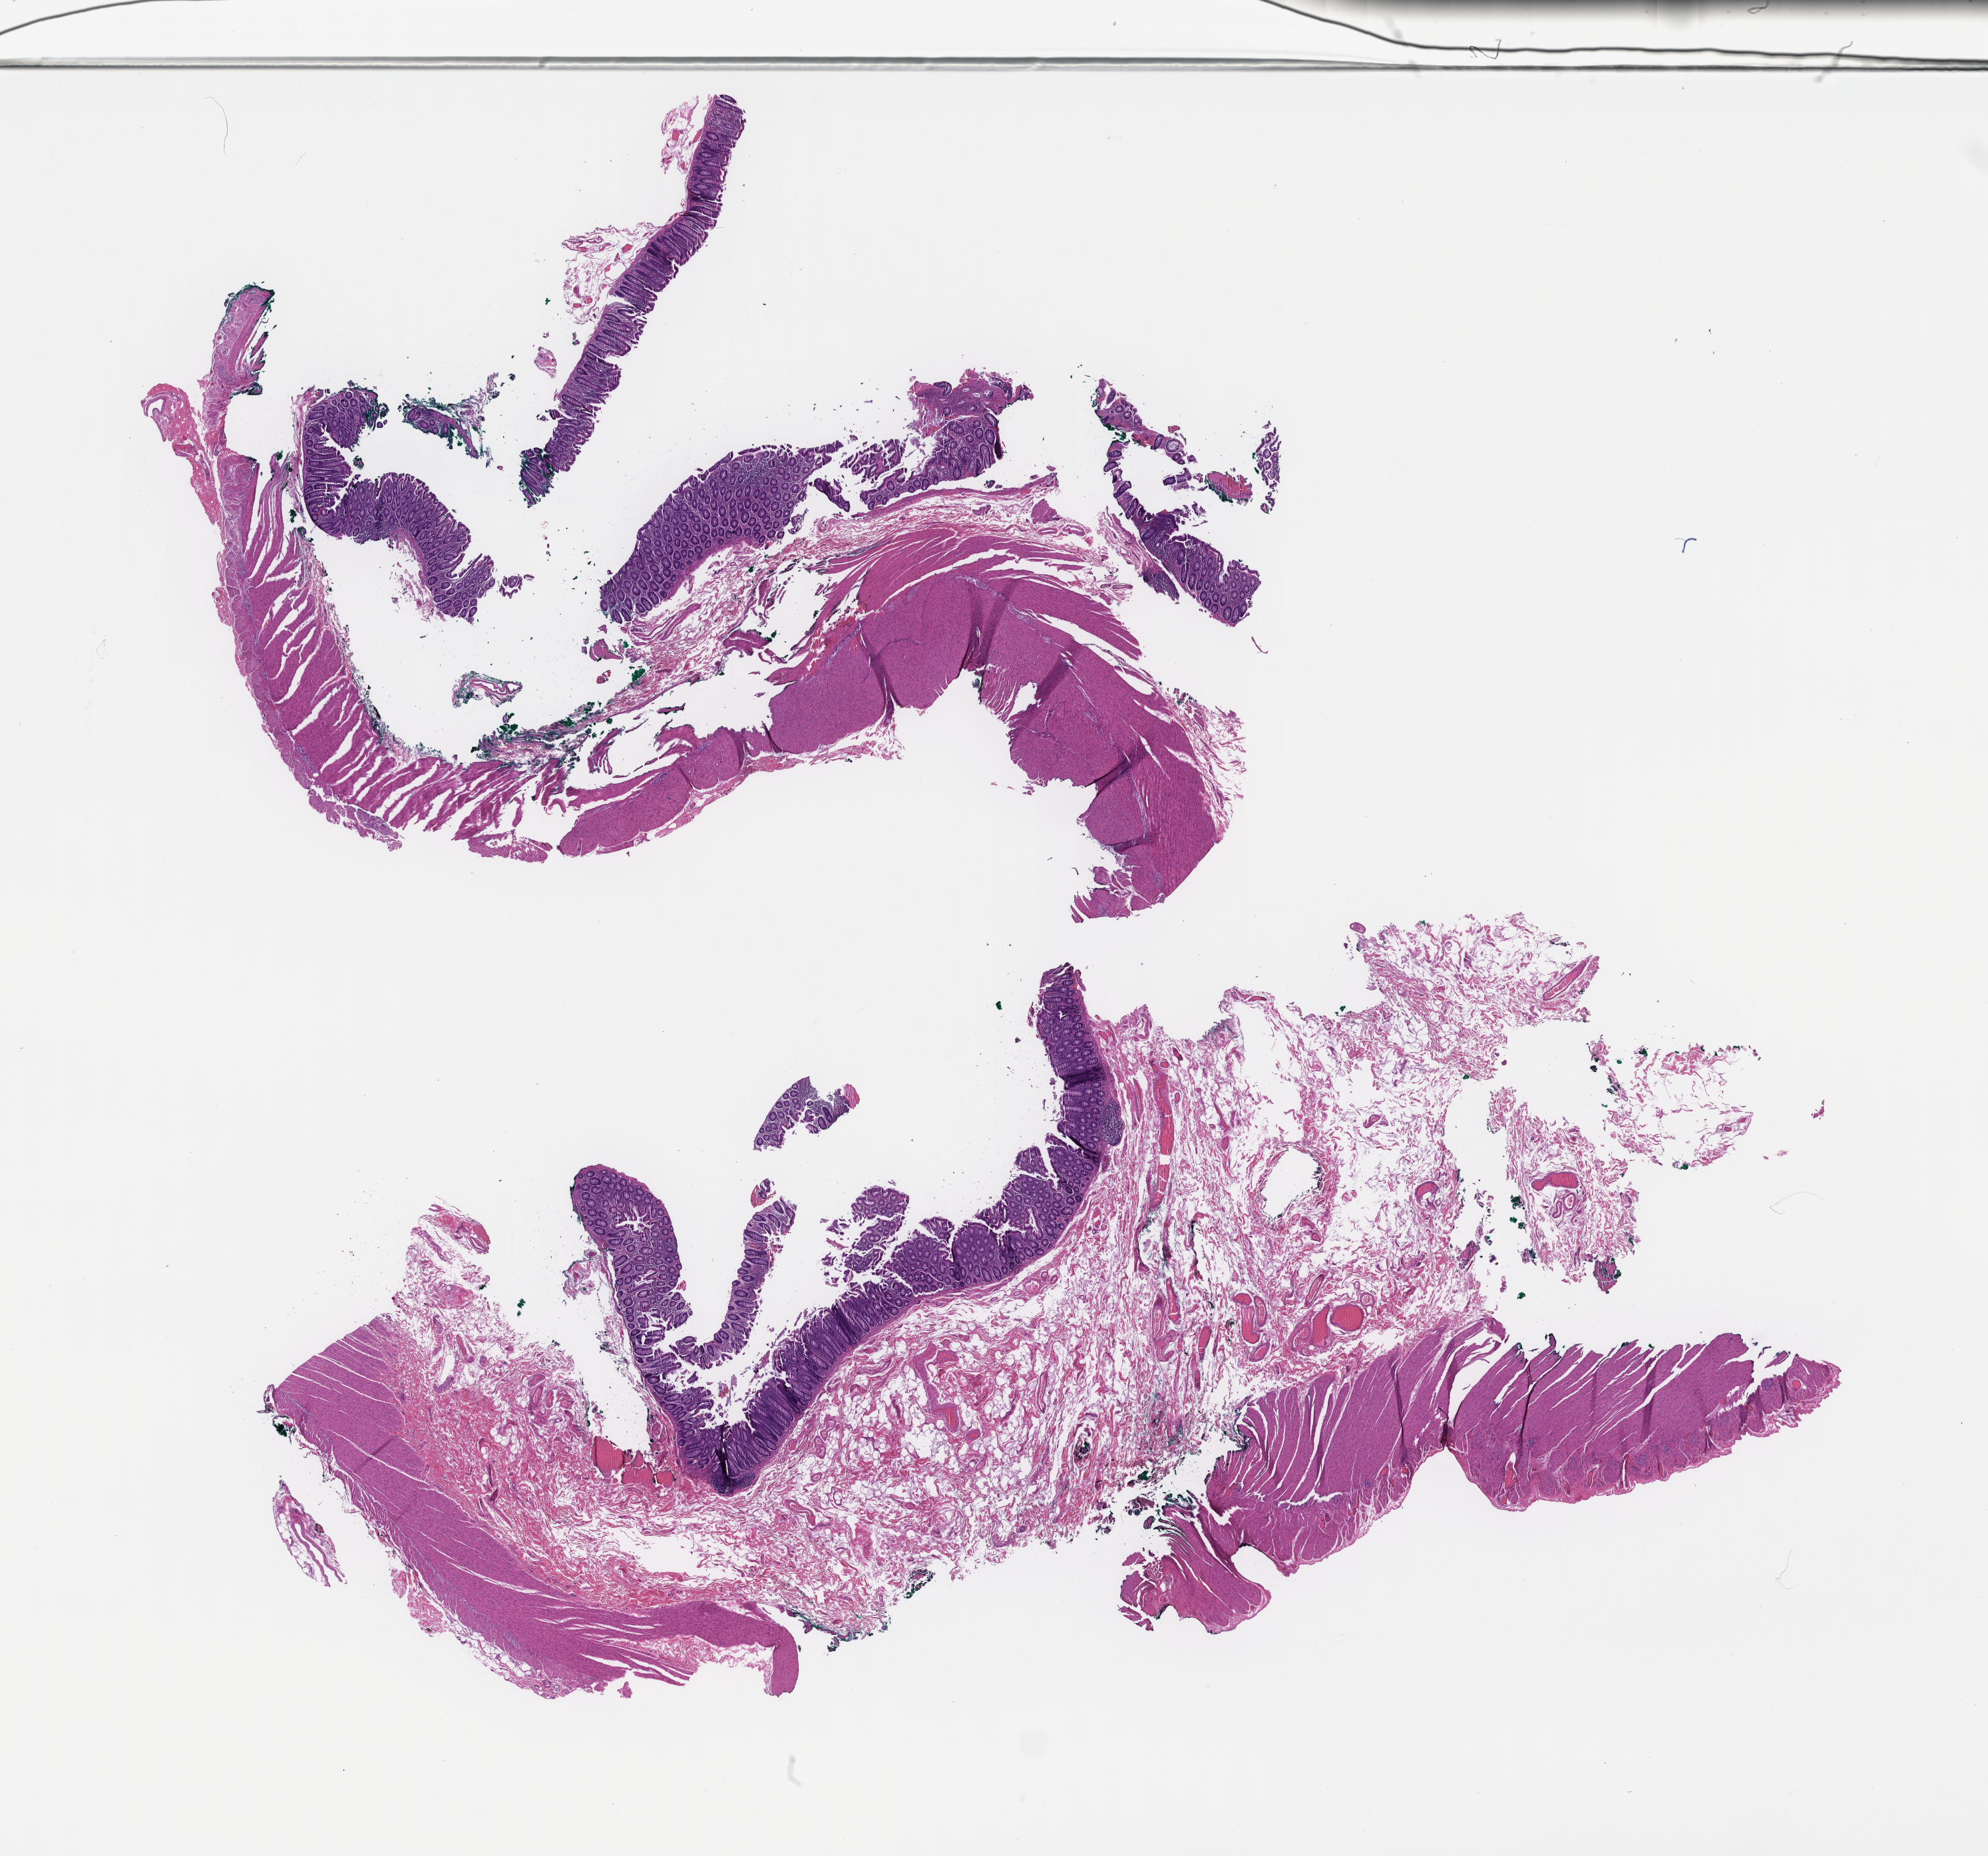
Whole-slide image, haematoxylin and eosin stain — a low-resolution overview of the entire scanned area, about 24.1 x 22.5 mm, FFPE section, site: colon, specimen time point: archival tissue. Male patient.
This section: primary tumor. Diagnosis: Colorectal Carcinoma.